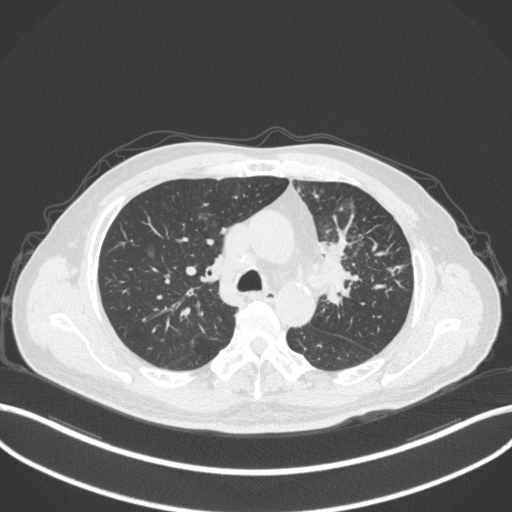
Chest CT, one axial slice. 120 kVp. Lung window (W 1500 / L -600 HU). 512 × 512 image matrix. Male patient, age 69 years. From the clinical record (not read from this slice): clinical TNM (as recorded): T2a N2 M0; histopathological grade: G2-3.
Outlined on this slice (rectangle marked by the reading radiologist):
- lung tumour (recorded histology: adenocarcinoma): bounding box <320,230,355,307> (left, top, right, bottom; pixels)